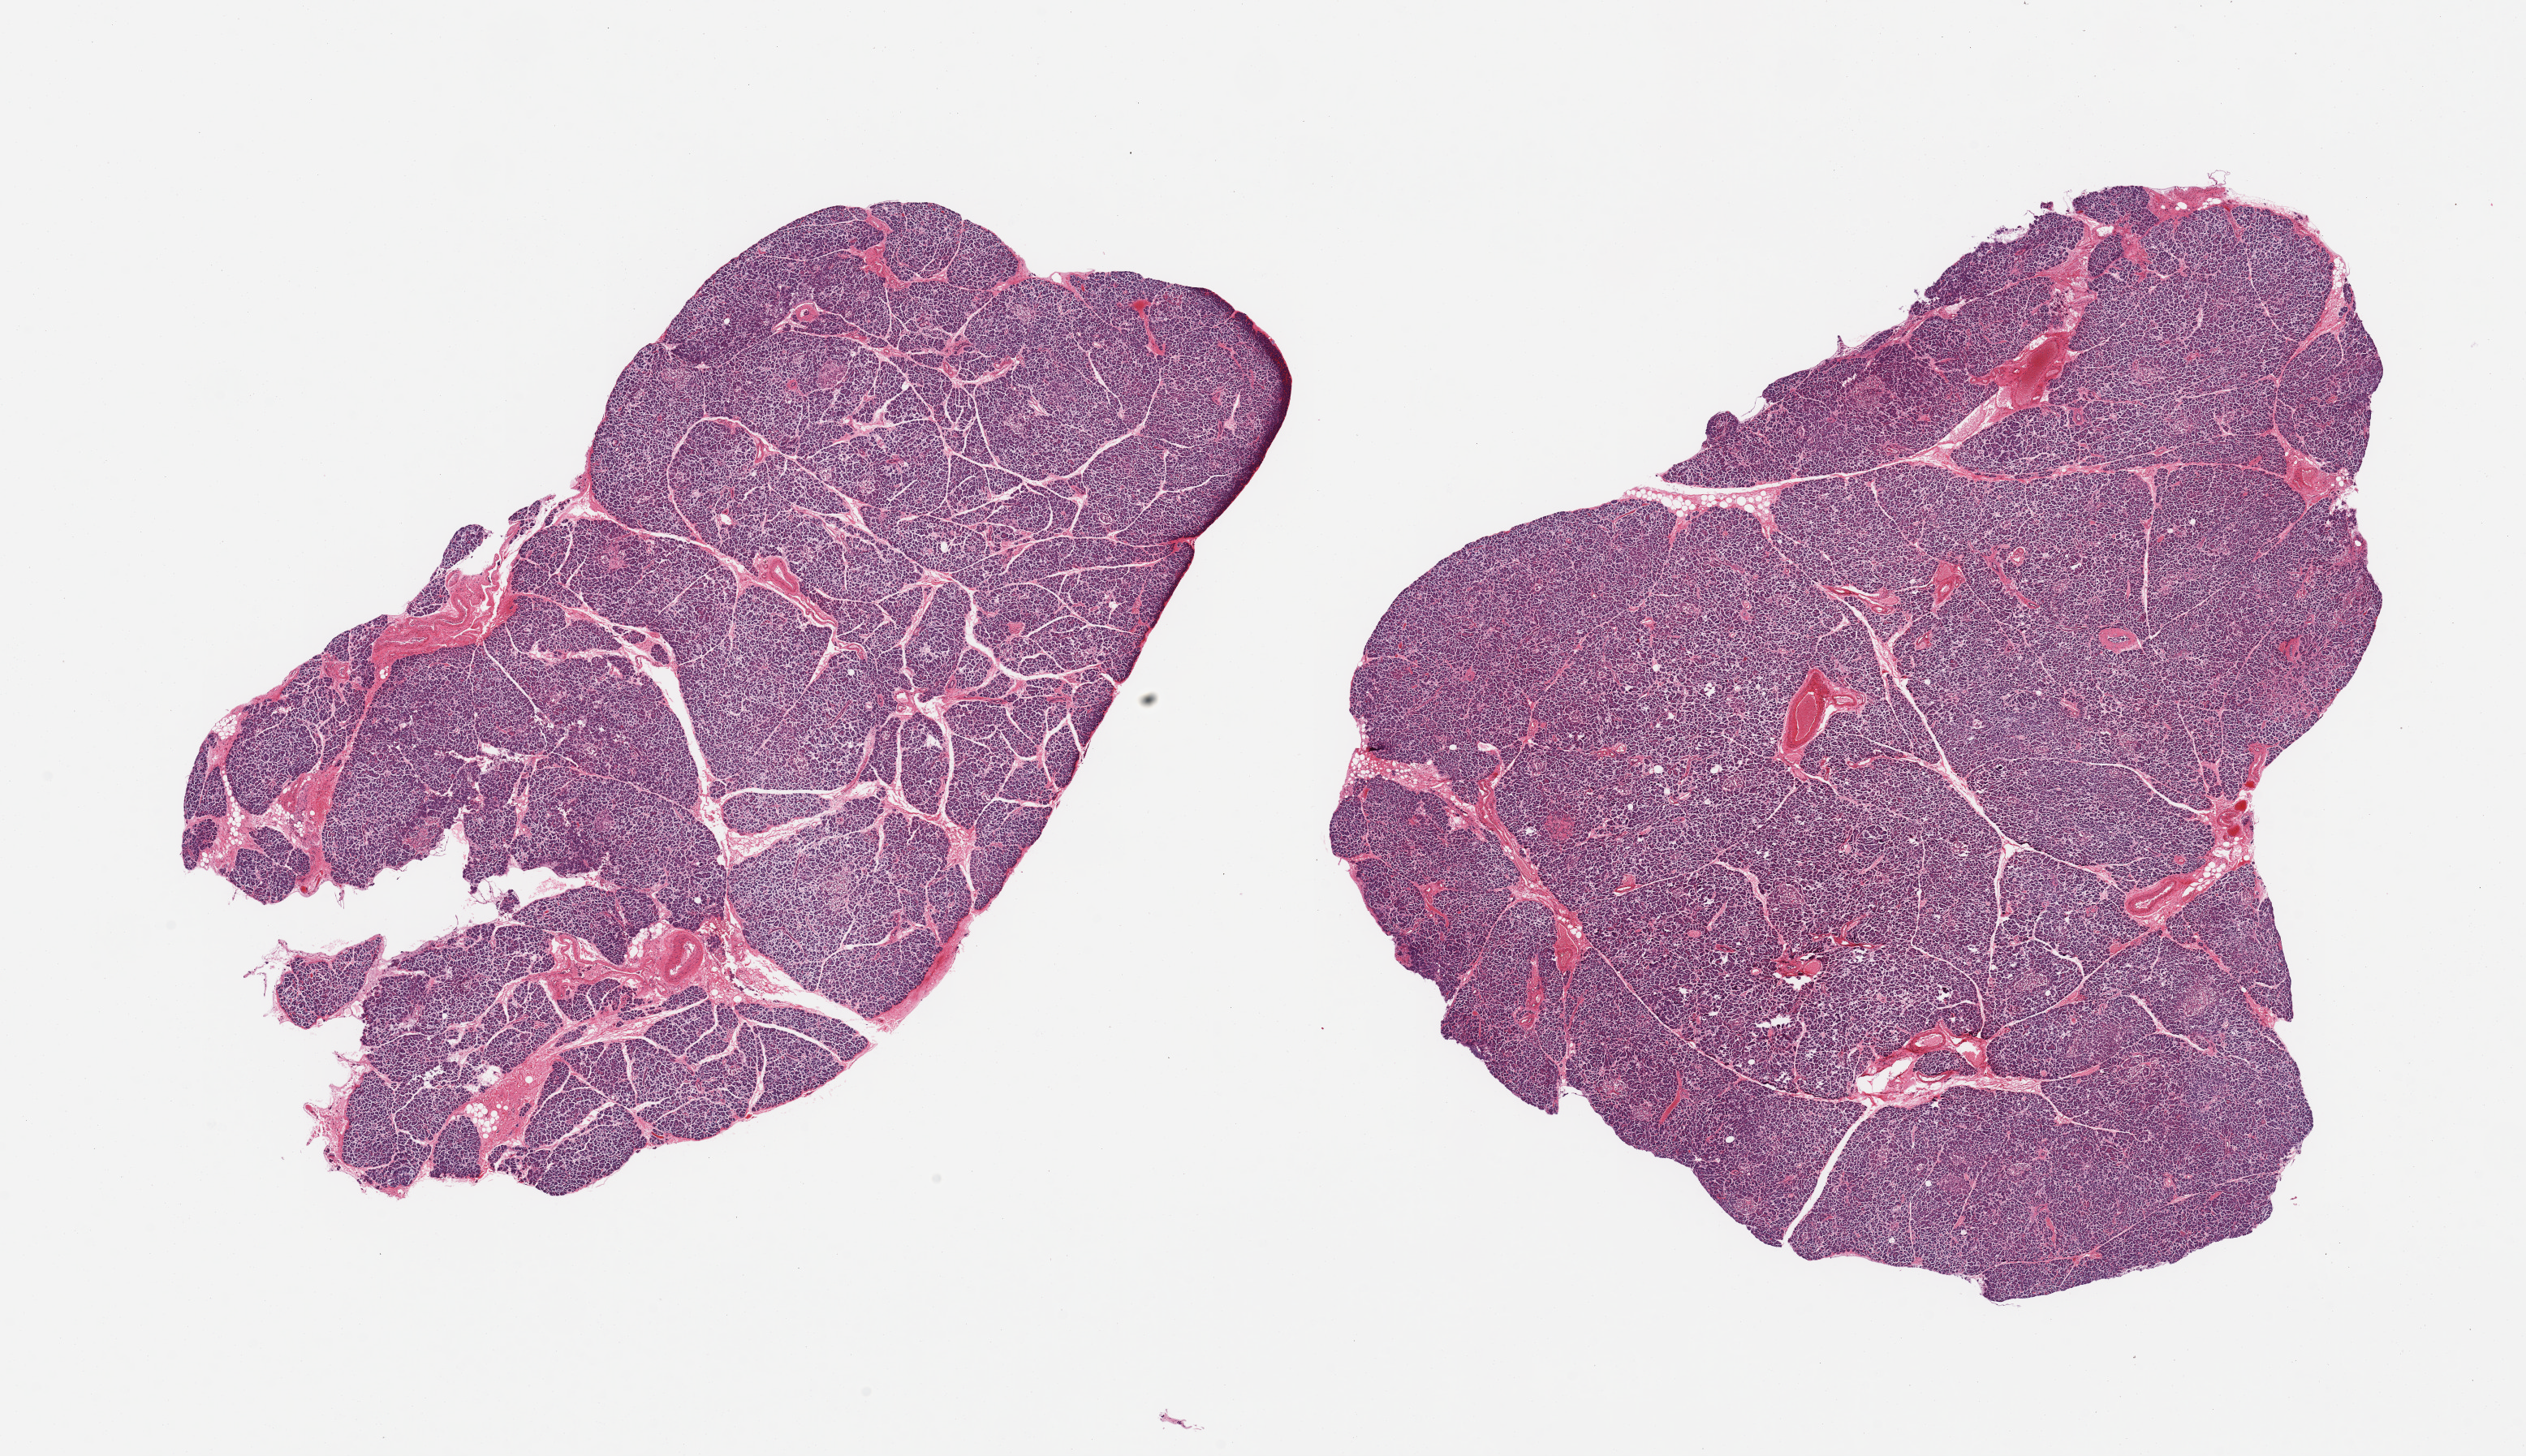
Haematoxylin and eosin whole-slide image, shown as a low-resolution overview of the whole scanned area (about 24.6 x 14.2 mm), PAXgene-fixed, paraffin-embedded tissue, sampled site (target tissue): pancreas, donor tissue sample.
Reviewer comment on this tissue sample: 2 pieces; well trimmed; virtually no internal or external fat.